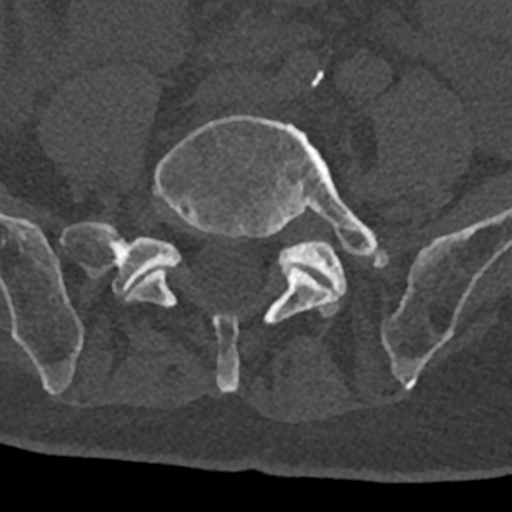
CT including the spine, one axial slice. Slice 186 of 797 in the series (ordered by position). Reconstruction kernel Br40s/3. 120 kVp. Bone window (W 1800 / L 400 HU). 512 × 512 image matrix, field of view 160 × 160 mm. Male patient, age 74 years. From the clinical record (not read from this slice): primary cancer: renal; vertebrae with lytic lesions (as recorded): T10, L1, L2, L3, L4, L5.
Annotated regions visible in this slice (semi-automatic segmentation, software-assisted and operator-edited):
- L4 vertebra: bounding box (x1, y1, x2, y2) in pixels: (311, 70, 324, 88)
- L5 vertebra: (127, 115, 380, 393)